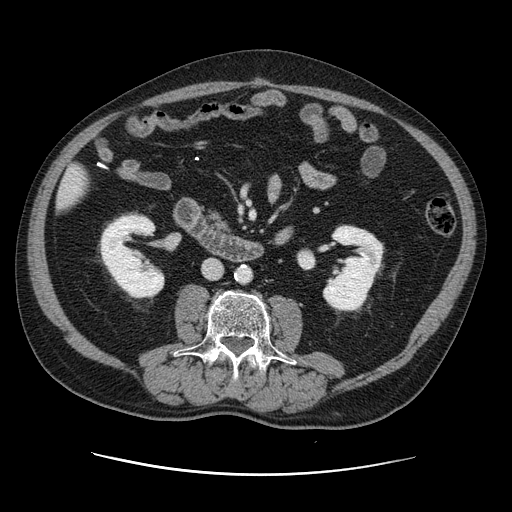
Contrast-enhanced abdominal CT, one axial slice. Position 30 of 141 along the scan axis. 120 kVp. Intravenous contrast given. Soft-tissue window (W 400 / L 40 HU). 512 × 512 image matrix, field of view 395 × 395 mm. Male patient, age 72 years. Case-level facts recorded for this patient, not image findings: diagnosis: colorectal cancer liver metastases, imaged before liver resection; multiple liver metastases: yes; largest metastasis: 5.4 cm.
Outlined on this slice (outlined manually by an expert reader):
- liver: box from (x=59, y=167) to (x=89, y=208) px
- planned liver remnant (the part of the liver to remain after resection): (x=59, y=167)–(x=88, y=208)